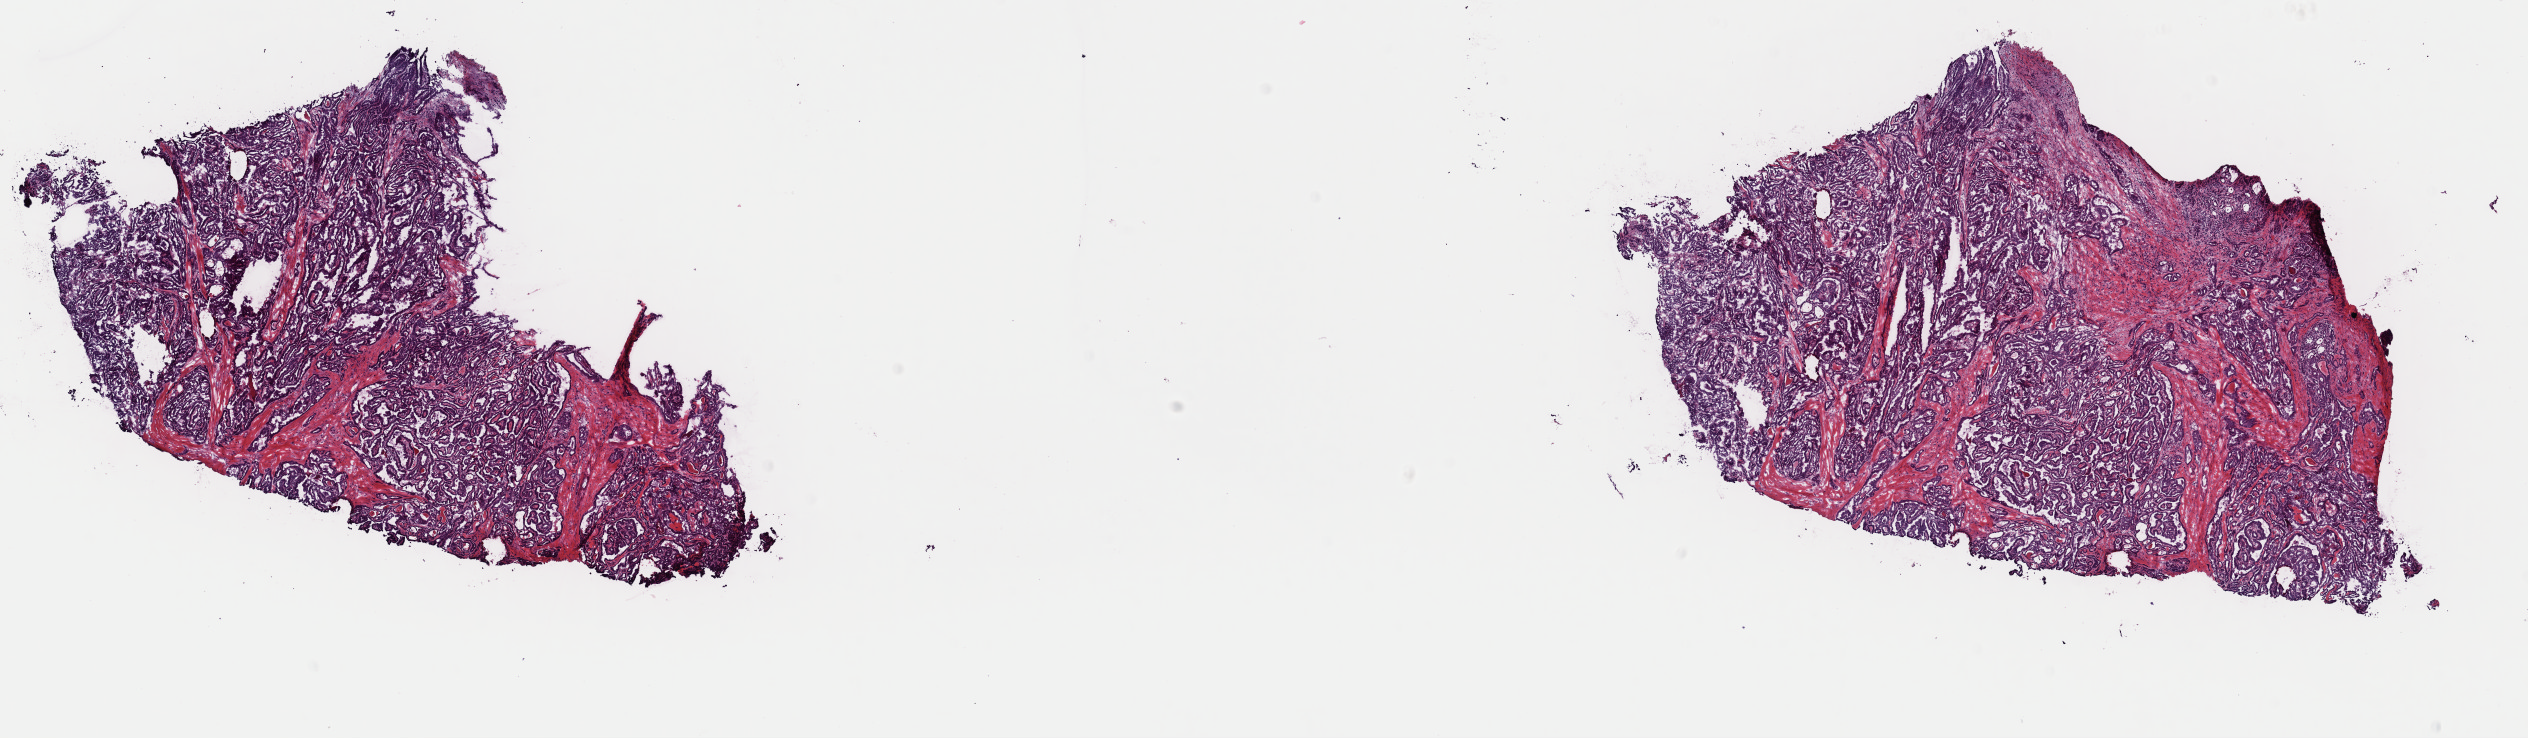
Digitized H&E tissue section (whole slide), whole scanned area (about 20.0 x 5.8 mm) shown as a low-resolution overview; frozen section from the top of the tissue portion; primary tumour sample from the thyroid. Female patient; age at initial diagnosis 55 years. Pathologist review of this section (percent, as recorded): tumour cells 60%, tumour nuclei 95%, normal cells 5%, stromal cells 35%, necrosis 0%. Infiltration values recorded for this section: lymphocyte infiltration 3%, monocyte infiltration 1%, neutrophil infiltration 0%.
• AJCC pathologic stage: IVA (7th edition)
• lymph nodes positive (case pathology): 2 of 3 examined
• pathologic diagnosis: Papillary adenocarcinoma, NOS (thyroid gland)